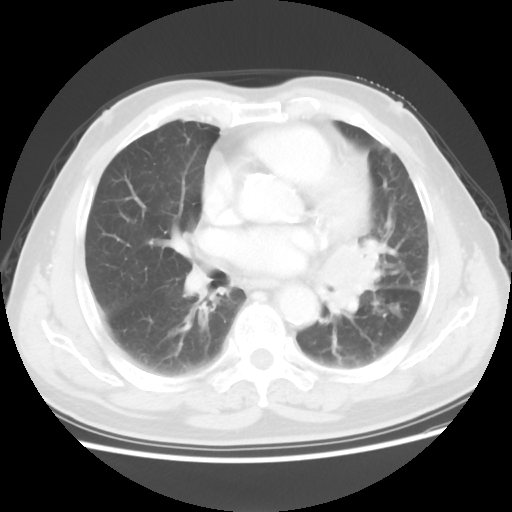
Chest CT, one axial slice; position 30 of 56 along the scan axis; reconstruction kernel STANDARD; 120 kVp; lung window (W 1500 / L -600 HU); 5 mm slice thickness; 512 × 512 image matrix, field of view 360 × 360 mm. Male patient, age 75 years. Case-level facts recorded for this patient, not image findings: clinical TNM (as recorded): T3 N0 M0.
Annotated regions visible in this slice (rectangle marked by the reading radiologist):
- lung tumour (recorded histology: squamous cell carcinoma): bounding box [x1, y1, x2, y2] px = [316, 233, 384, 316]